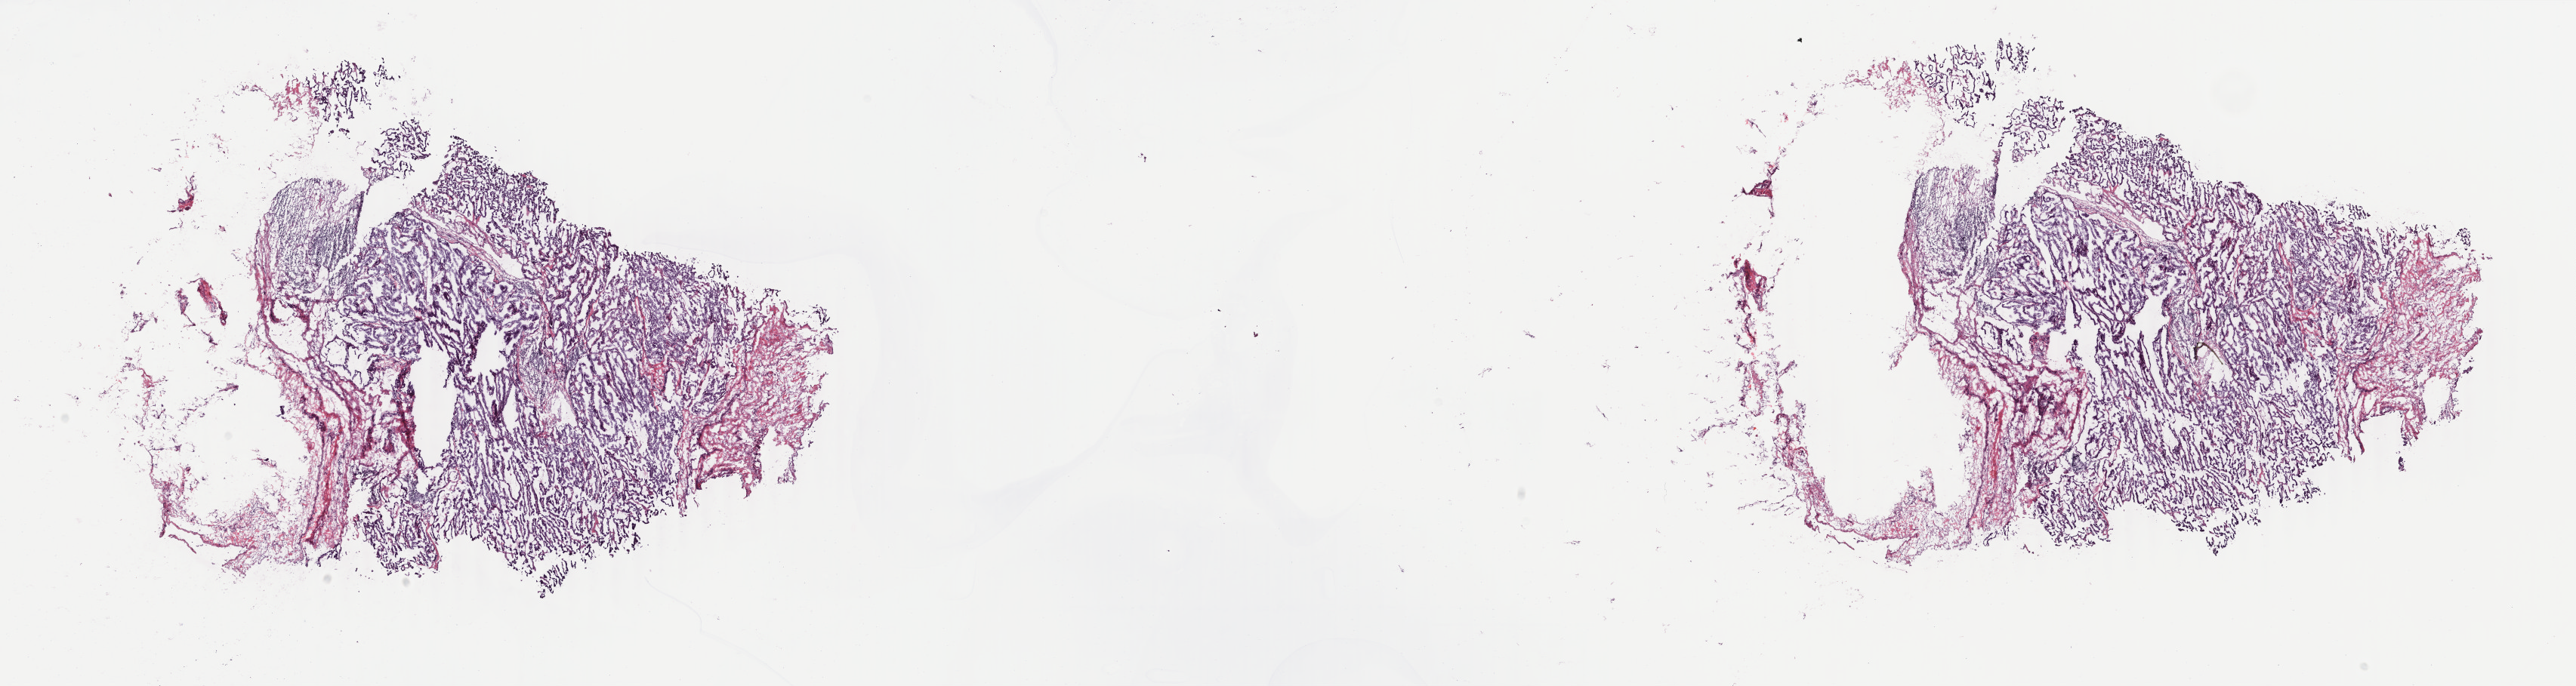
Digitized H&E tissue section (whole slide), shown as a low-resolution overview of the whole scanned area (about 27.1 x 7.2 mm, acquisition: 40x scan), frozen section from the top of the tissue portion, metastatic tumour sample, sampled site not recorded. Male patient; age at initial diagnosis 71 years. Pathologist review of this section (percent, as recorded): tumour cells 80%, tumour nuclei 90%, normal cells 0%, stromal cells 20%, necrosis 0%. Infiltration values recorded for this section: lymphocyte infiltration 7%, monocyte infiltration 0%, neutrophil infiltration 0%.
• this section: metastatic tumour tissue
• patient diagnosis: Papillary adenocarcinoma, NOS (primary site: thyroid gland)